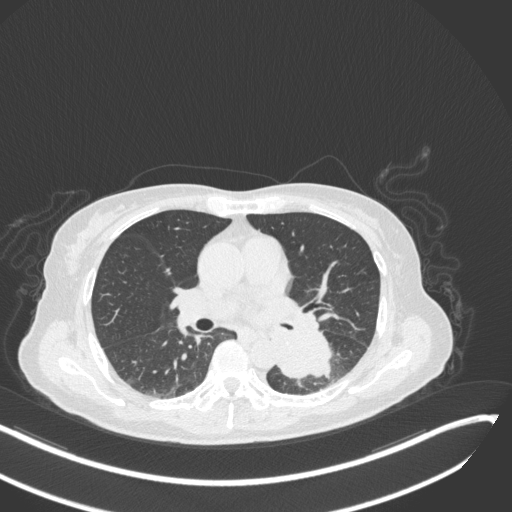
Chest CT, one axial slice; position 150 of 342 along the scan axis; reconstruction kernel B31f; 120 kVp; lung window (W 1500 / L -600 HU); 1 mm slice thickness; 512 × 512 image matrix. Patient: female, 64 years. From the clinical record (not read from this slice): clinical TNM (as recorded): T3 N1 M1.
Structures marked on this image (rectangle marked by the reading radiologist):
- lung tumour (recorded histology: small cell carcinoma): bounding box [x1, y1, x2, y2] px = [276, 325, 340, 380]